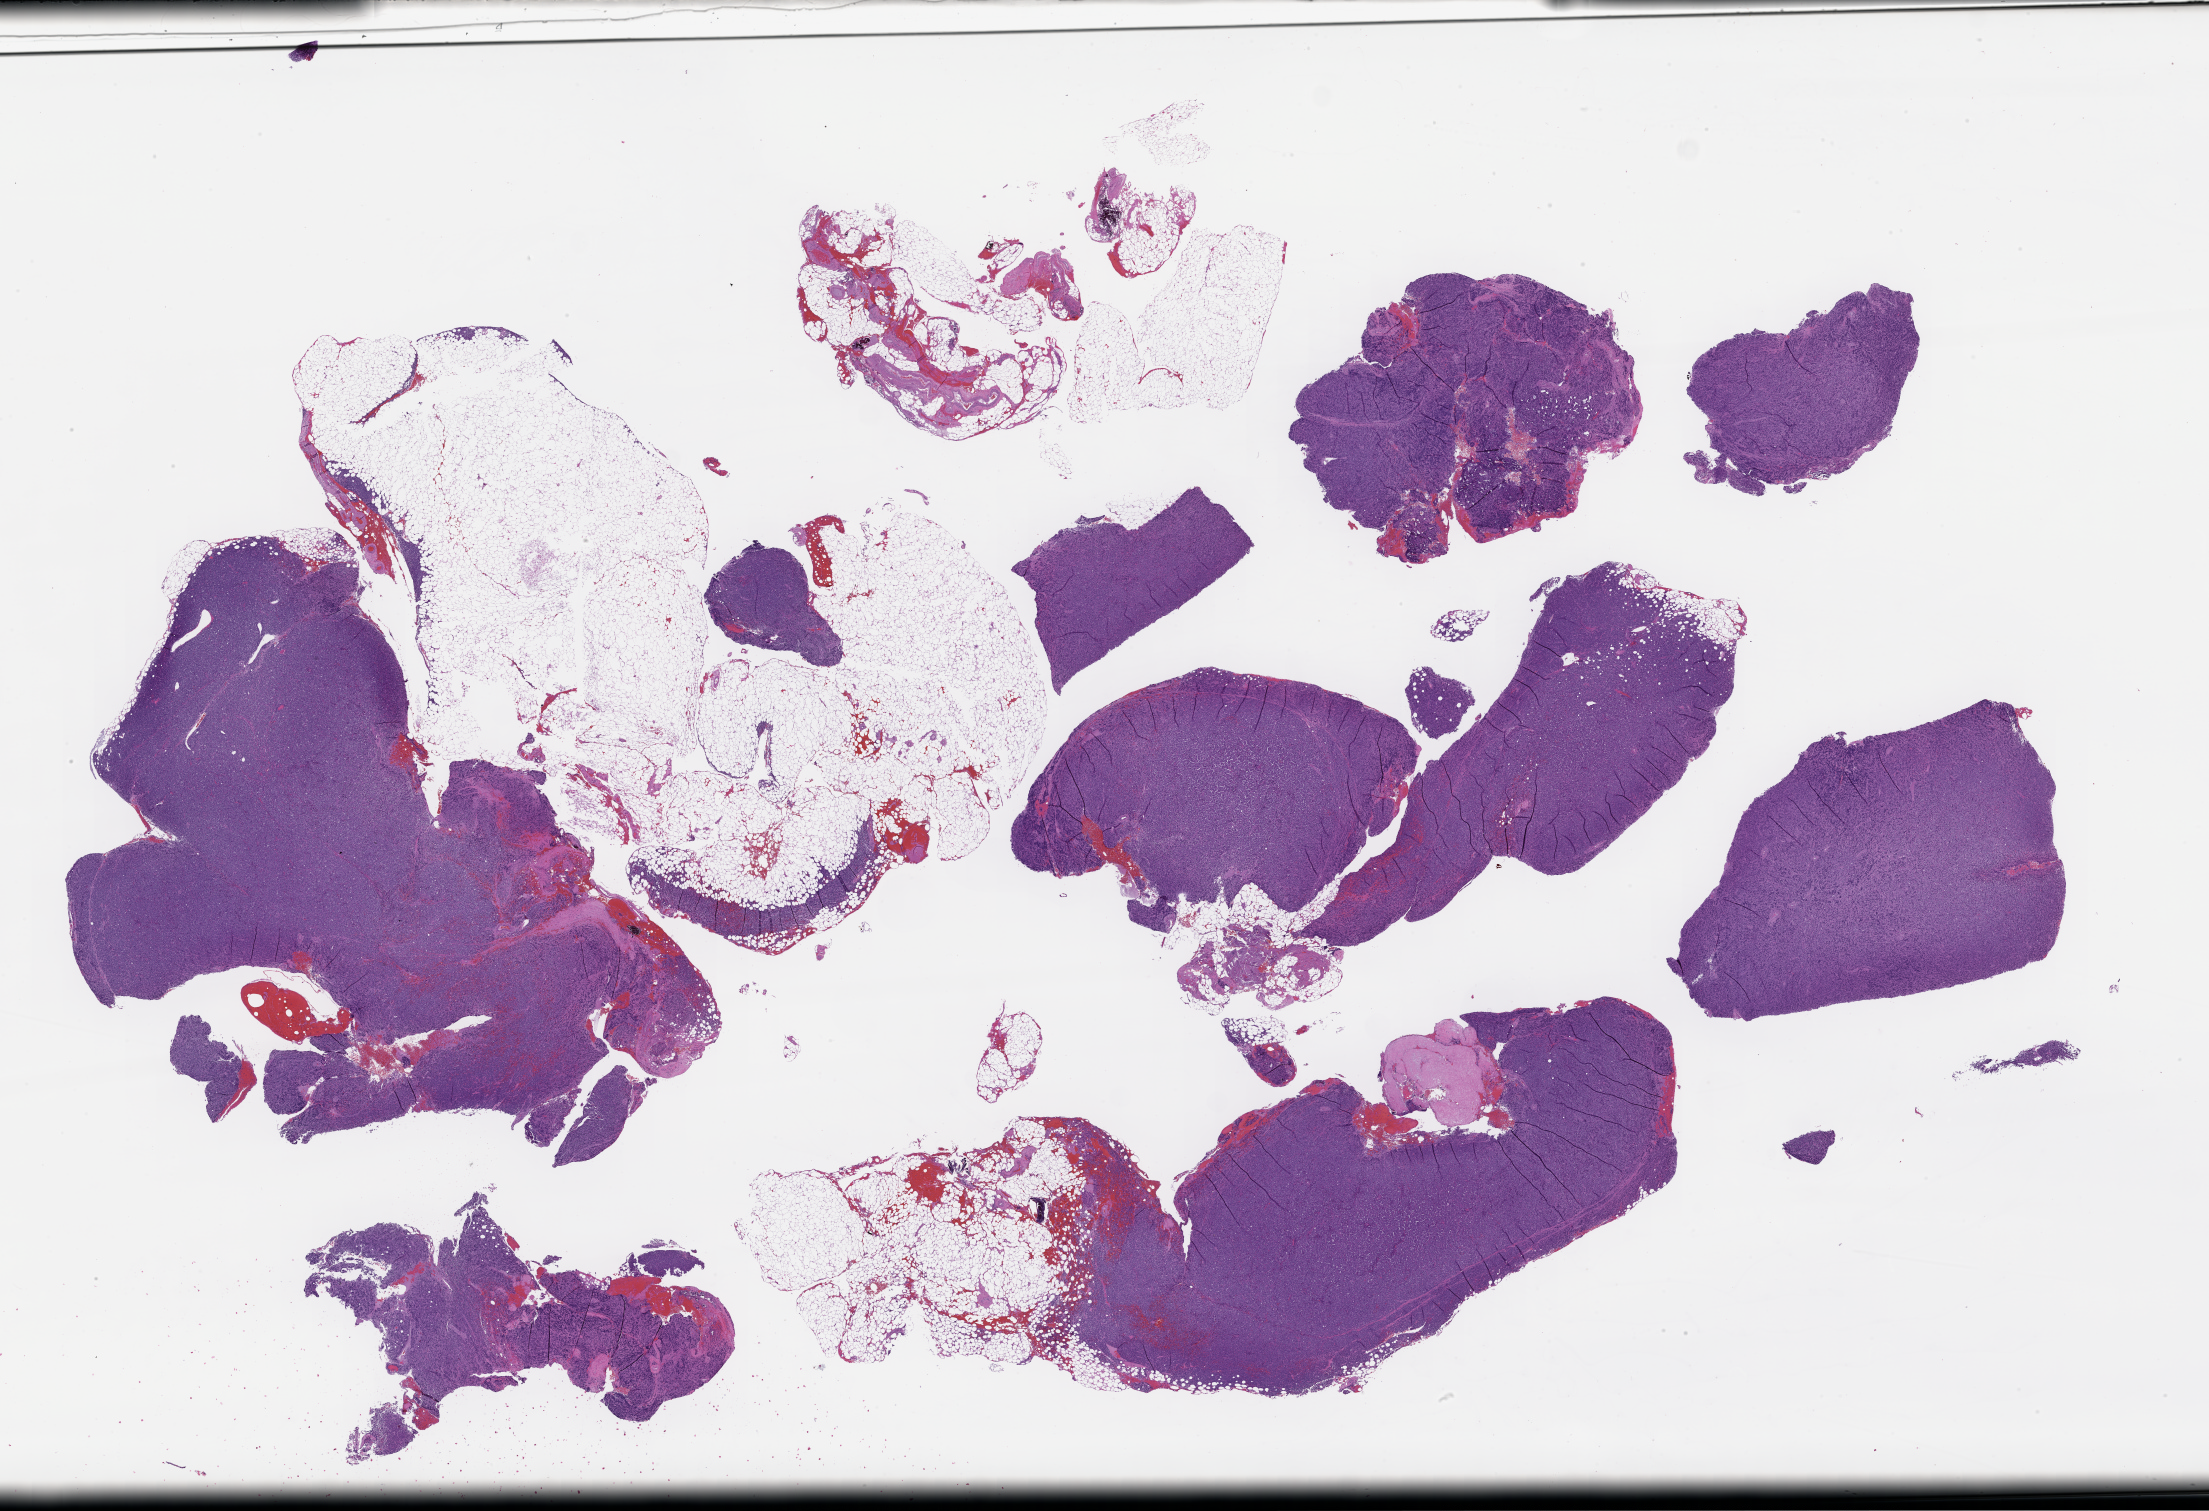
Digitized hematoxylin and eosin (H&E)-stained section, shown as a low-resolution overview of the whole scanned area (about 35.7 x 24.4 mm), formalin-fixed paraffin-embedded section, tissue site: bone marrow, specimen time point: collected at disease progression. Male patient.
* this section: primary tumor
* diagnosis: Plasma Cell Myeloma